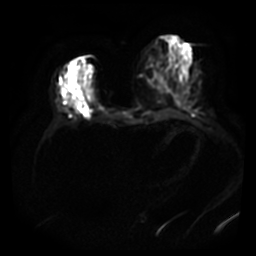
Breast MRI, one axial slice; position 16 of 40 along the scan axis; diffusion-weighted series; image 2 of 4 stored at this slice position (different b-values; order by instance number); 3 T; 5 mm slice thickness; 256 × 256 image matrix, field of view 380 × 380 mm. Female patient.
Structures marked on this image (expert manual segmentation):
- tumour on diffusion-weighted imaging: bounding box [x1, y1, x2, y2] px = [63, 95, 80, 108]